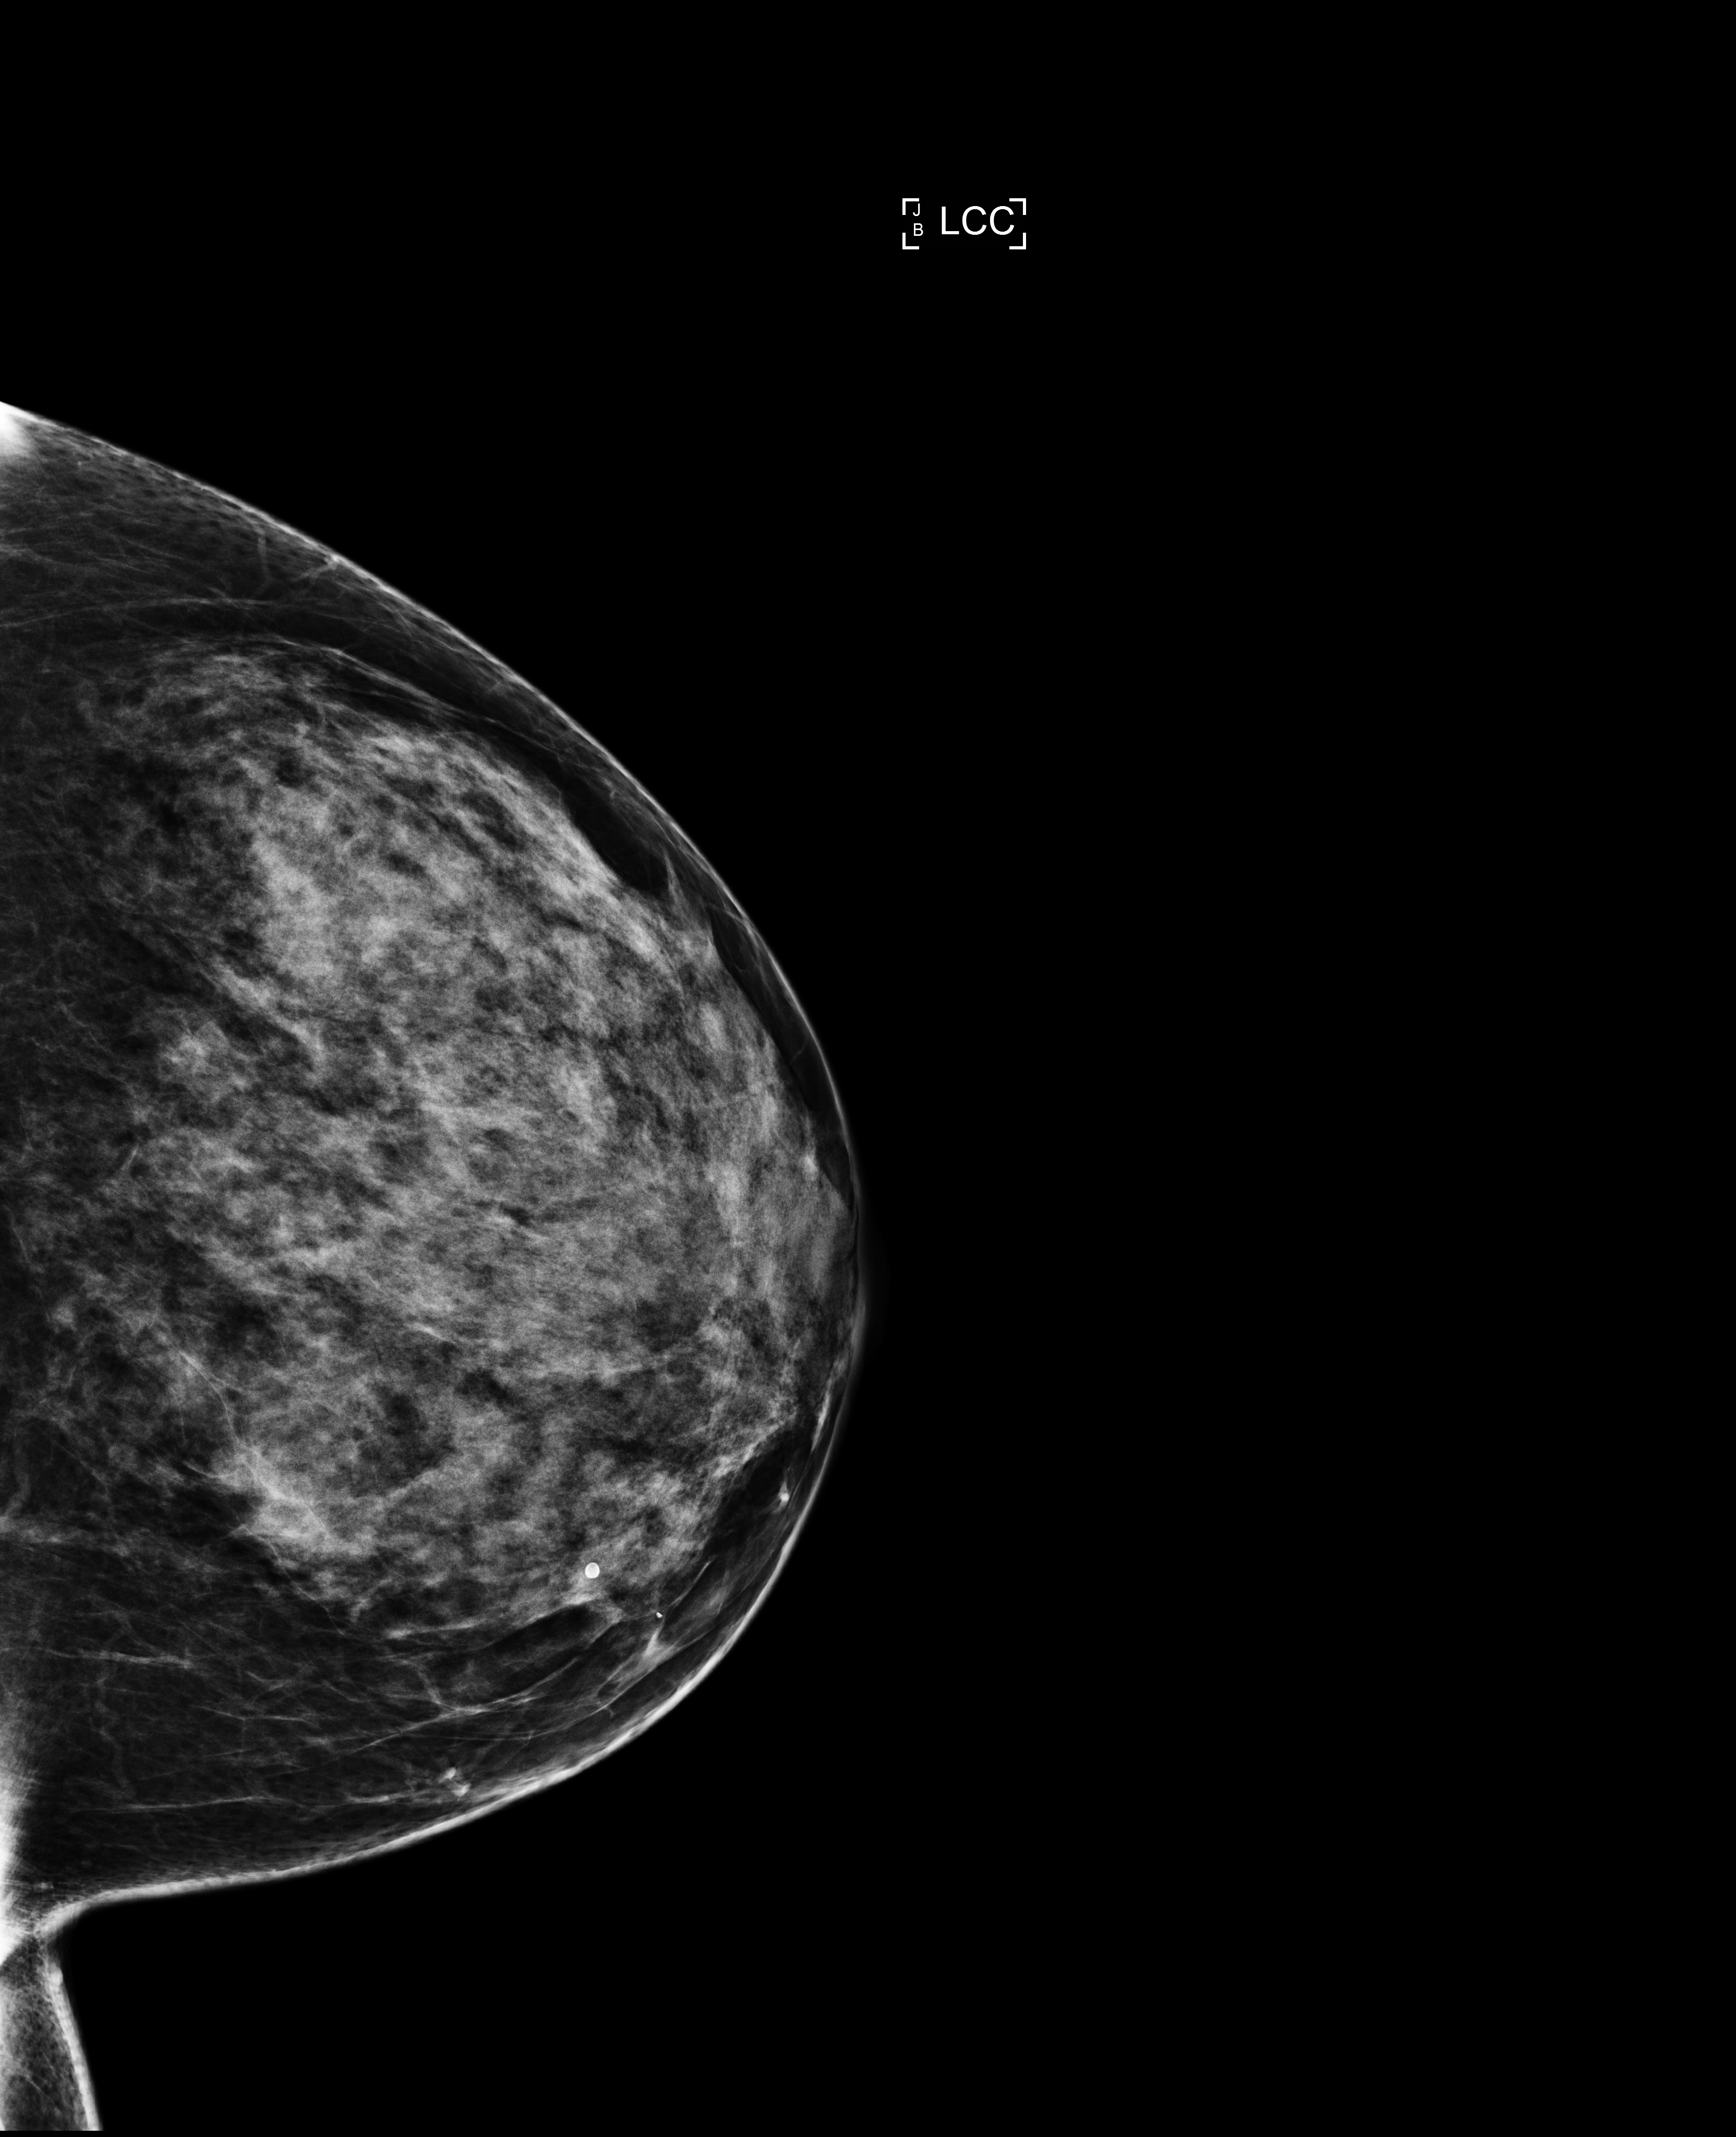
Screening examination, compressed breast thickness 60 mm. Patient aged 42 years (female).
Image type: full-field digital mammogram. Breast: left. Projection: CC view.